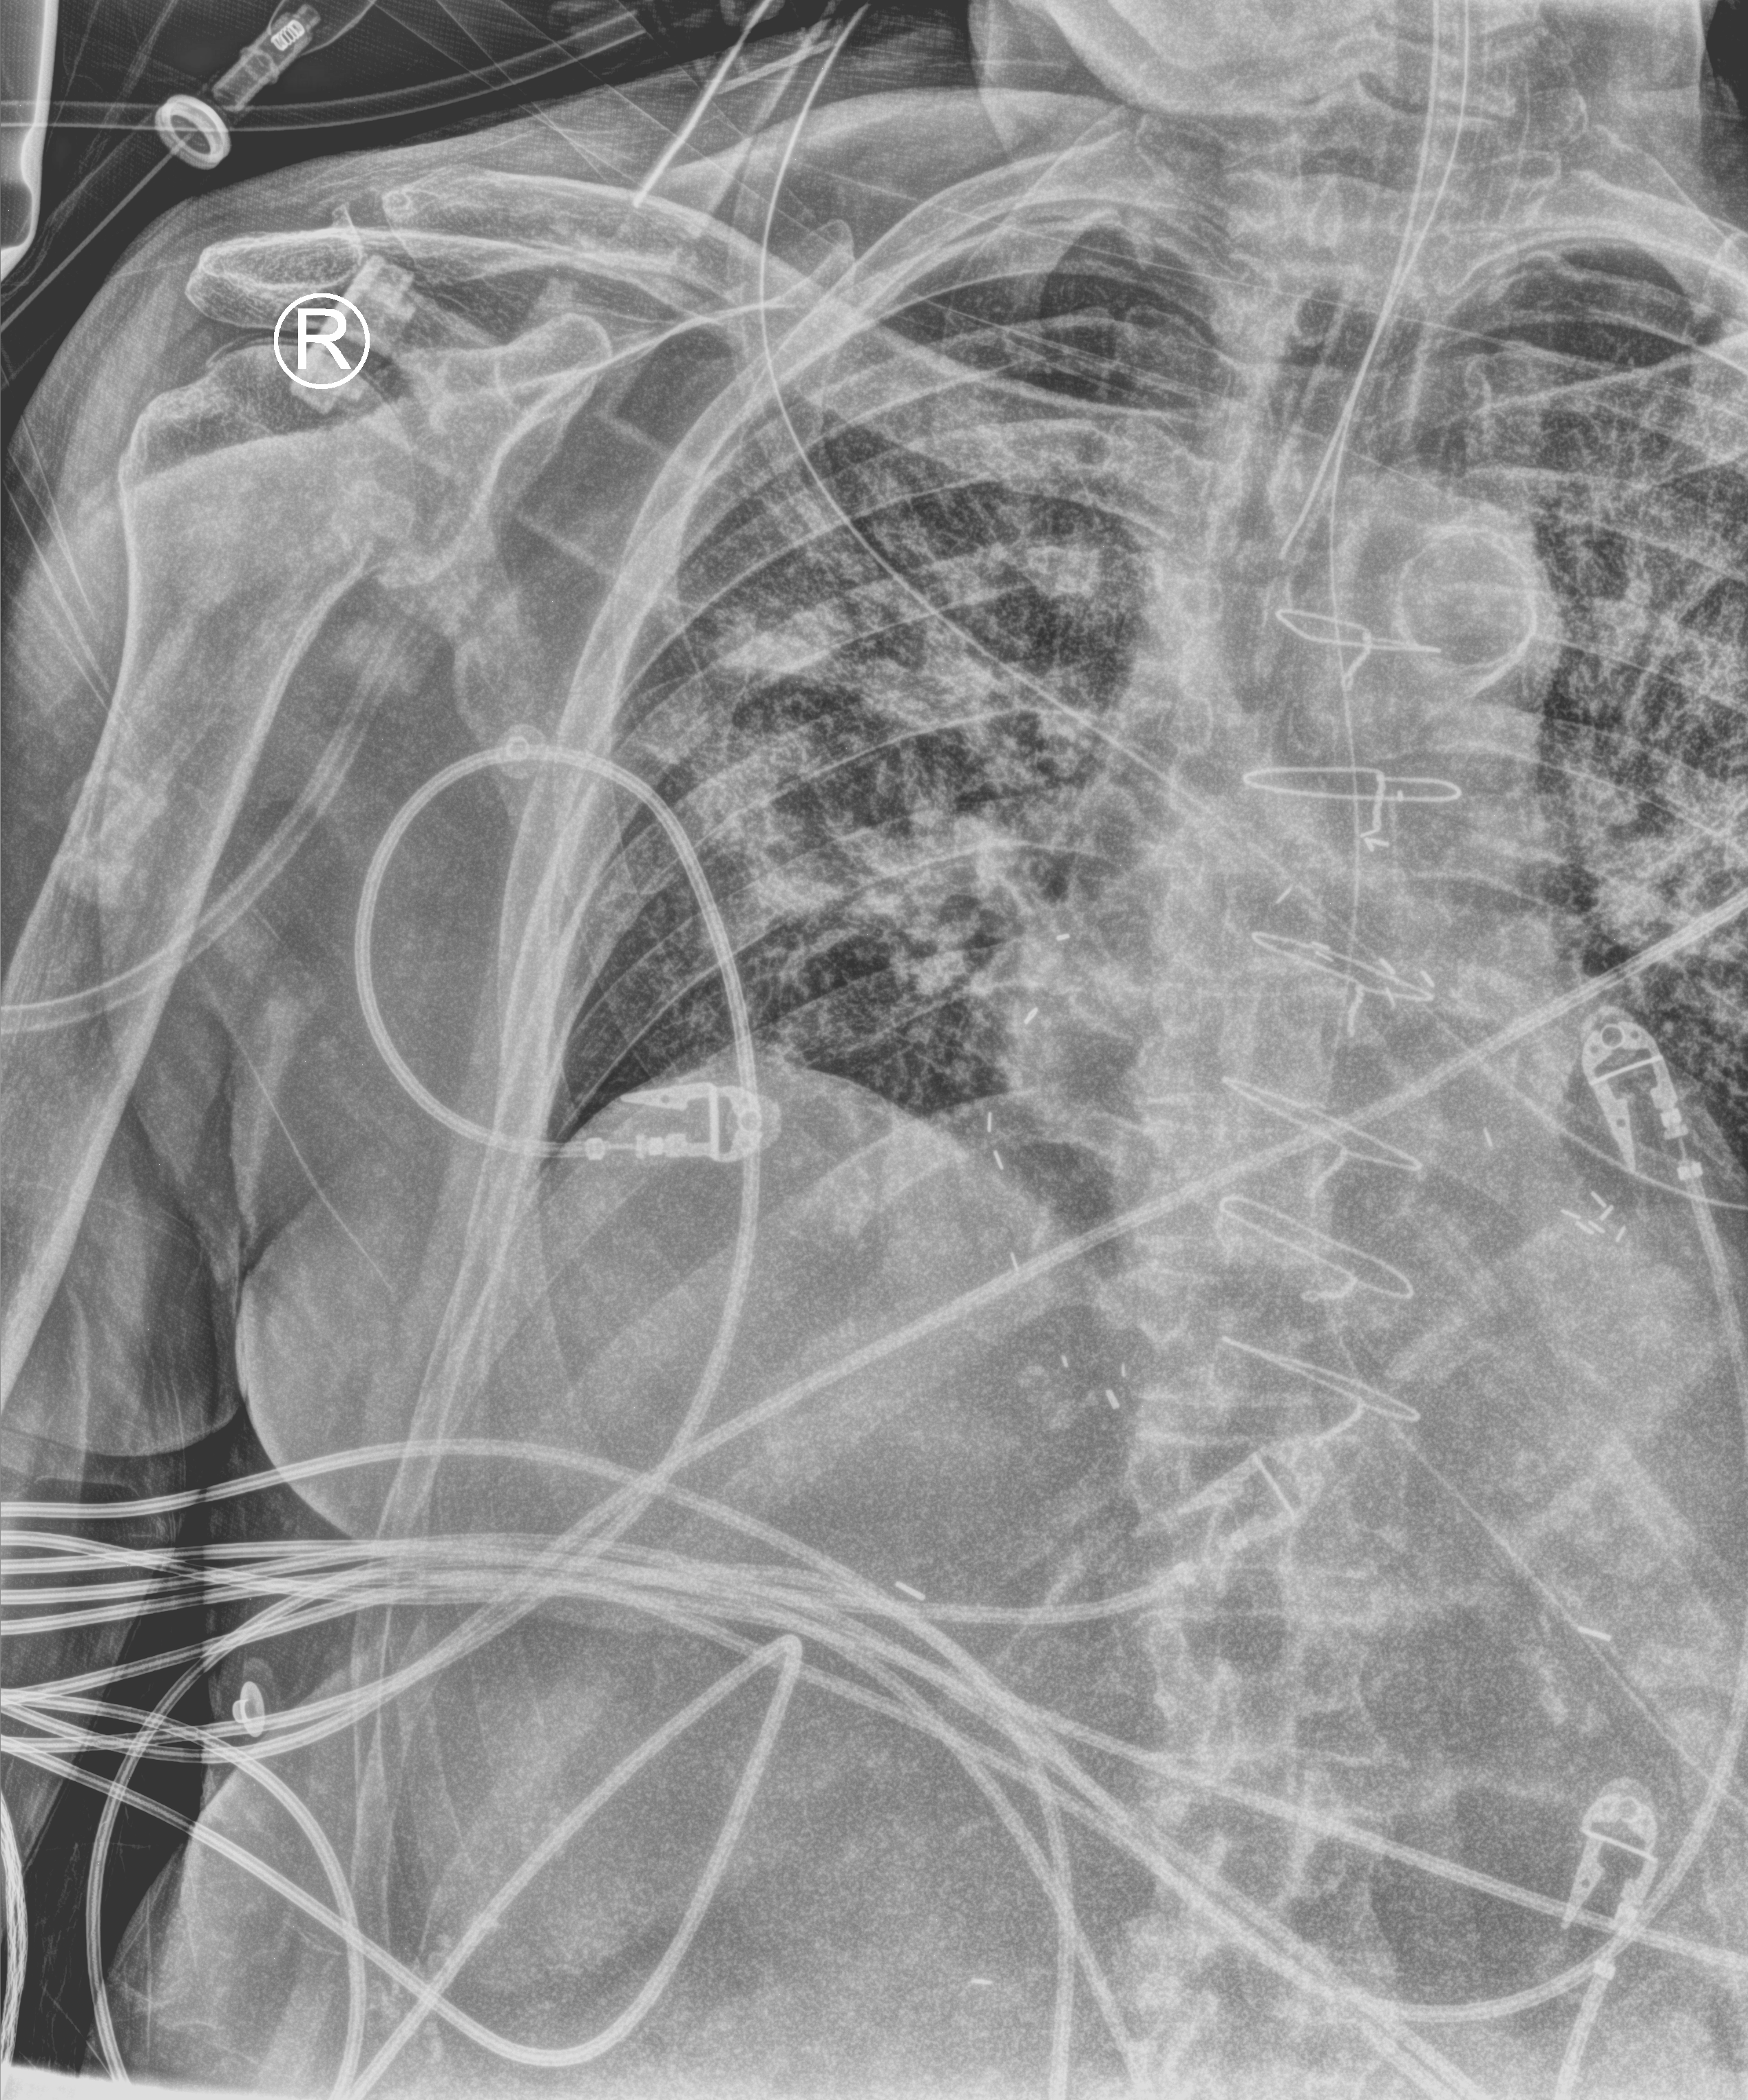
Portable chest radiograph. Patient hospitalised with COVID-19; male, aged 75–90 years.
Hospital-stay facts (about this admission, not read from this image; timing relative to this image not recorded):
- mechanically ventilated during this hospital stay: yes
- admitted to intensive care during this hospital stay: yes